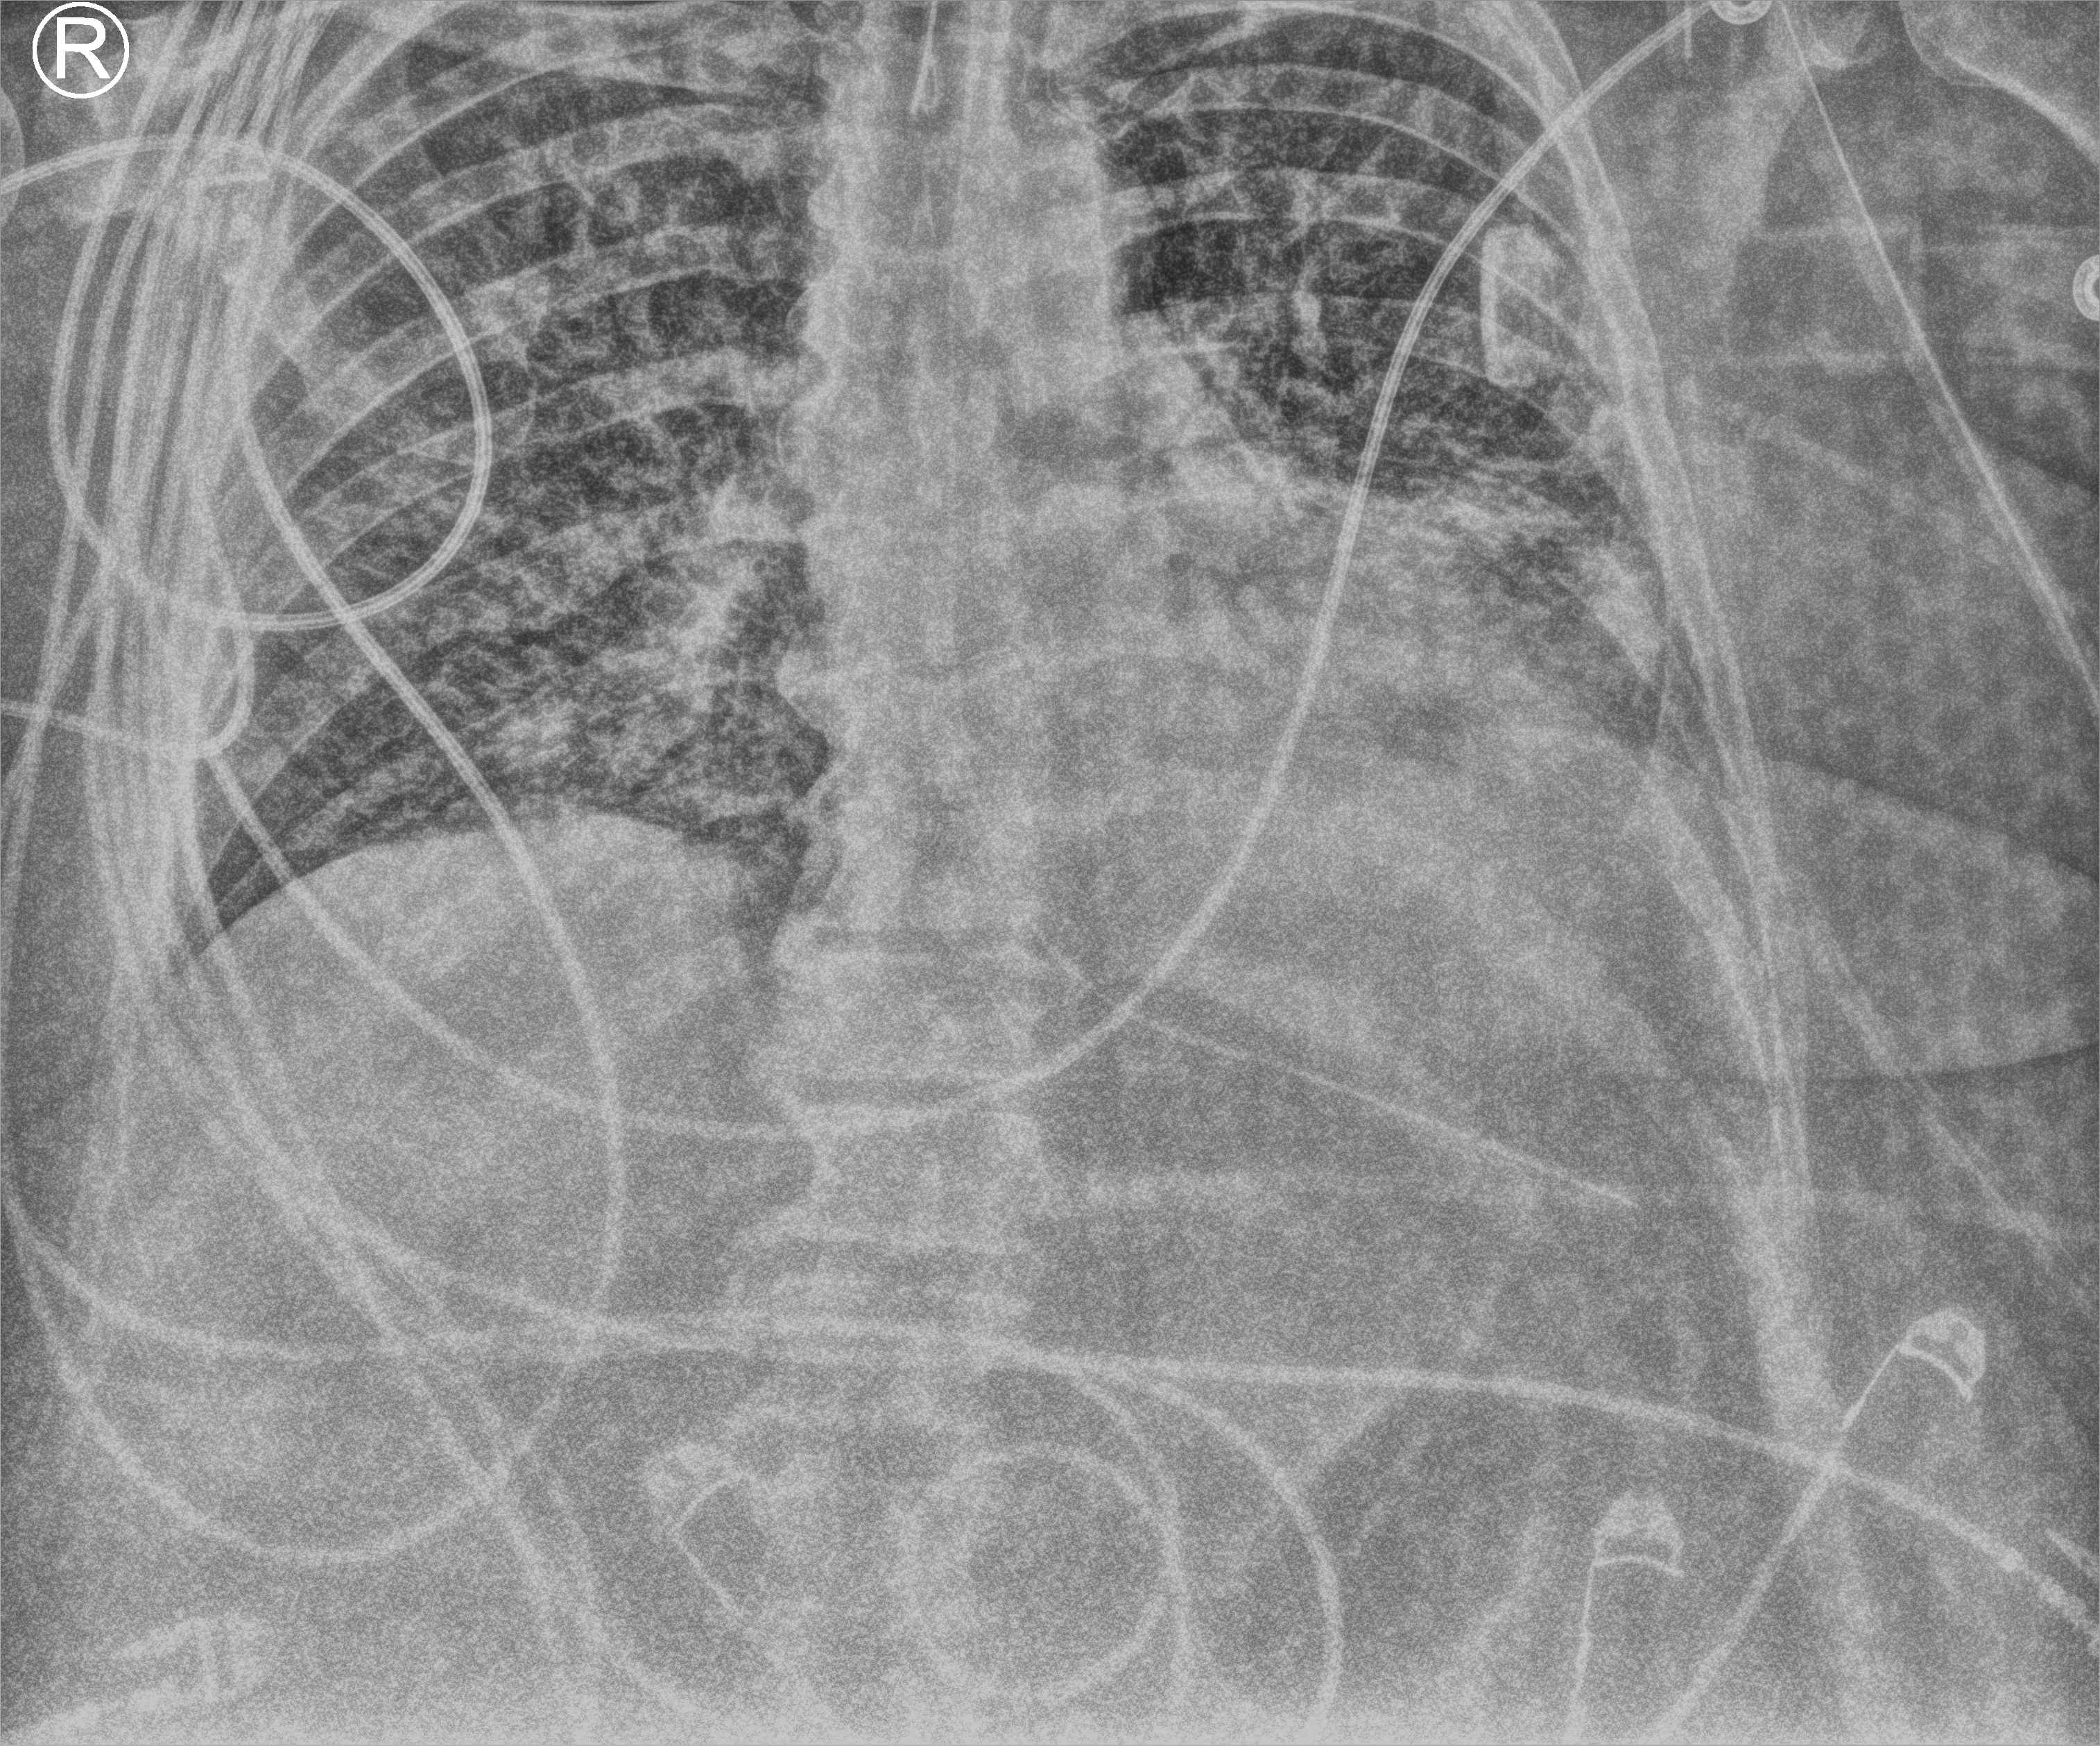
Chest X-ray (portable); anteroposterior (AP) projection. Adult patient hospitalised with COVID-19, age 18–59 years.
Hospital-stay facts (about this admission, not read from this image; timing relative to this image not recorded):
- mechanically ventilated during this hospital stay: yes
- admitted to intensive care during this hospital stay: yes